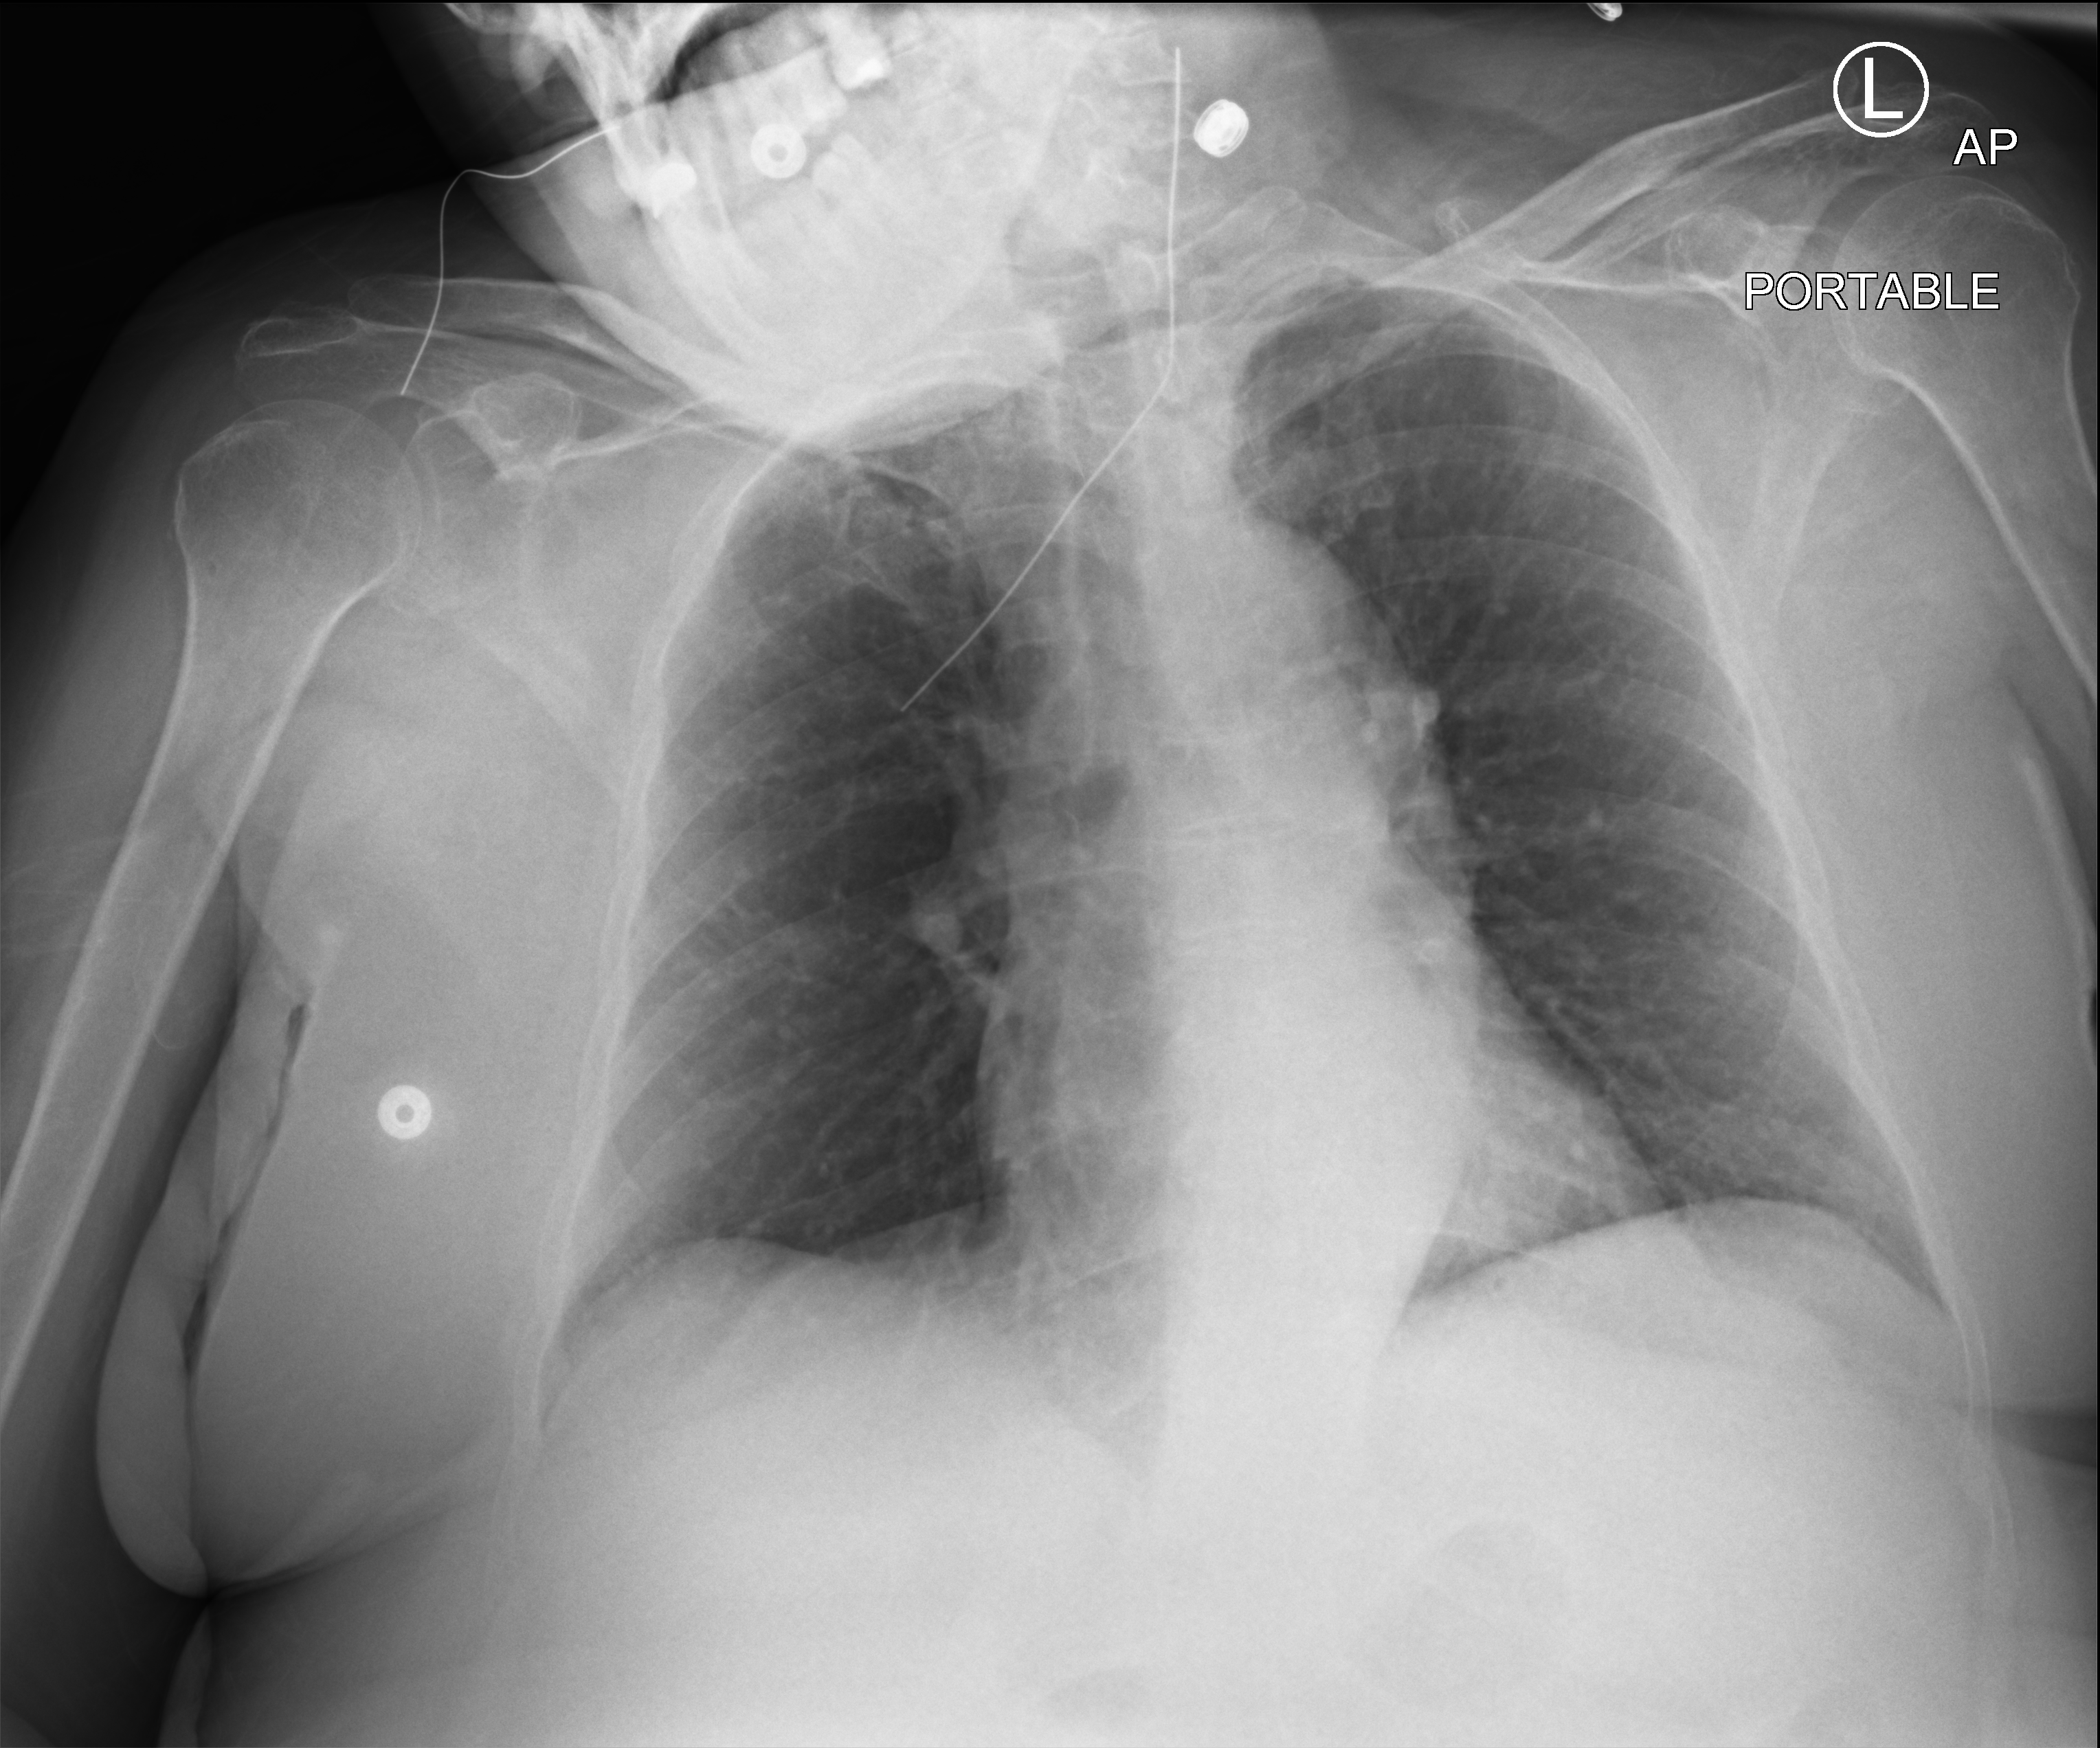
Chest X-ray (portable); anteroposterior (AP) projection. Patient hospitalised with COVID-19; female, aged 18–59 years.
From the hospital-stay record, not from the radiograph (when in the stay this image was taken is not recorded): mechanically ventilated during this hospital stay: no.